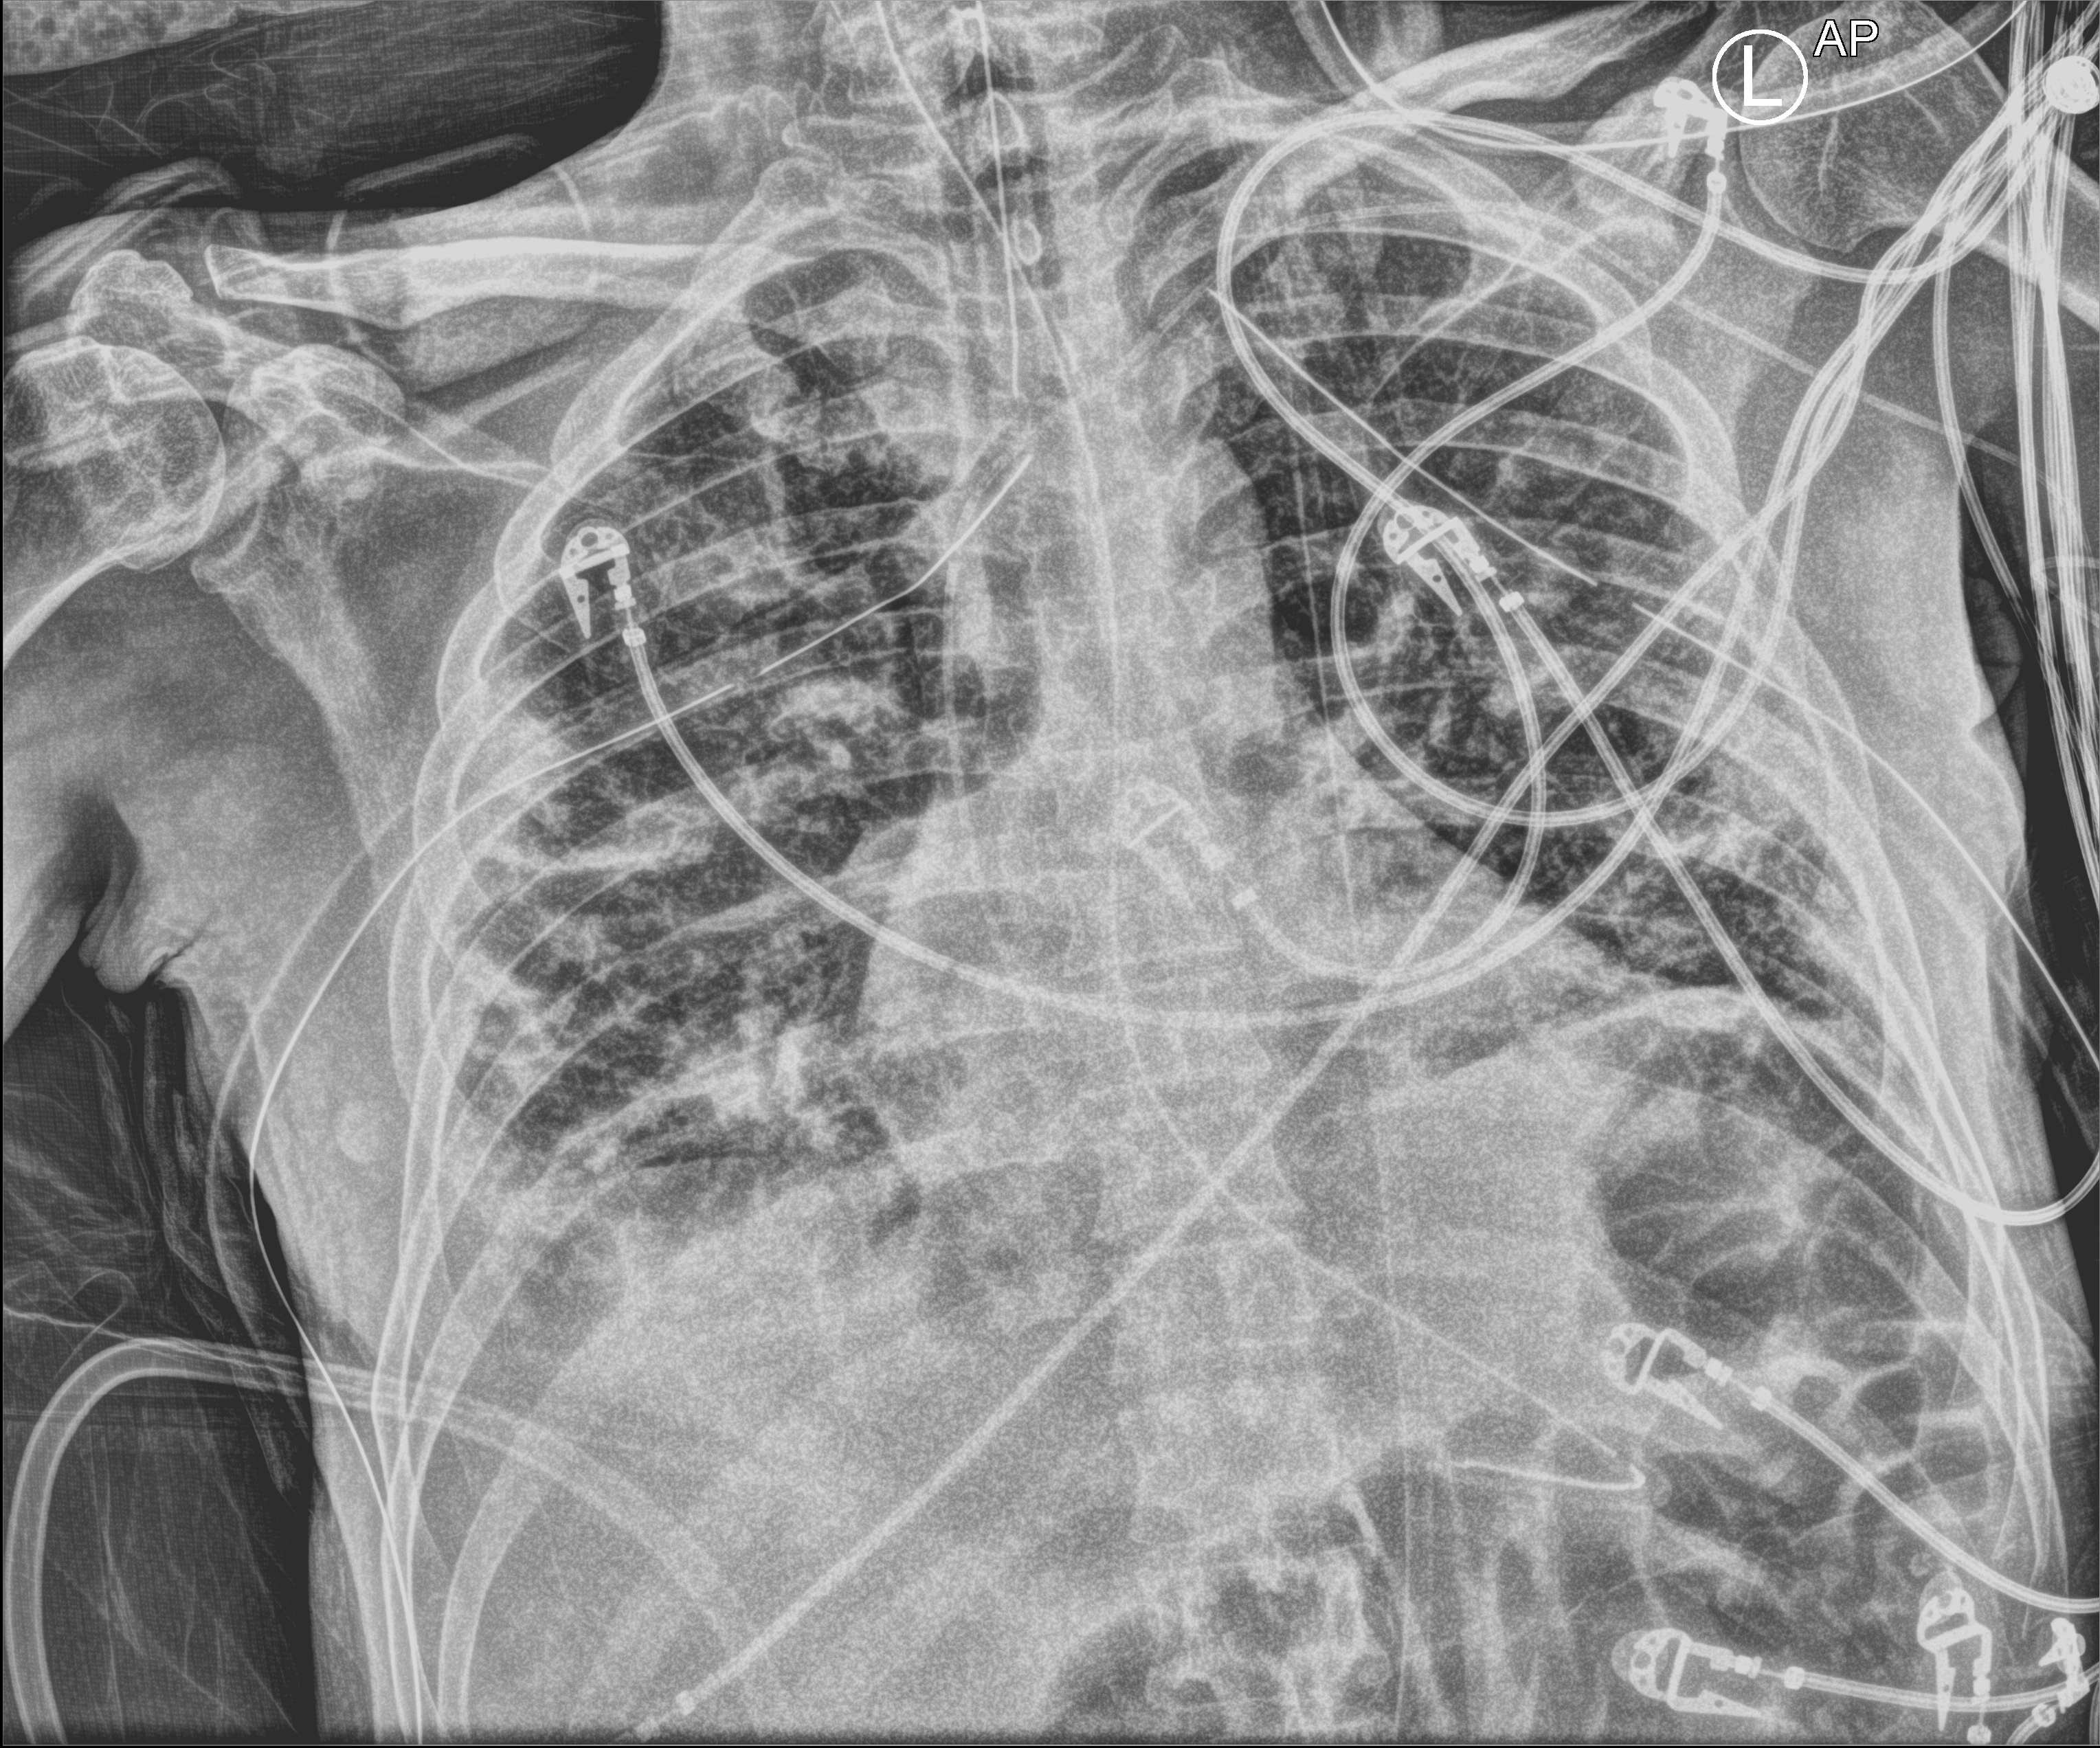
Portable chest radiograph, anteroposterior (AP) projection. Patient hospitalised with COVID-19; male, aged 18–59 years.
Admission-level facts for this patient (not findings on this image; timing relative to this image not recorded): length of hospital stay: 96 days.